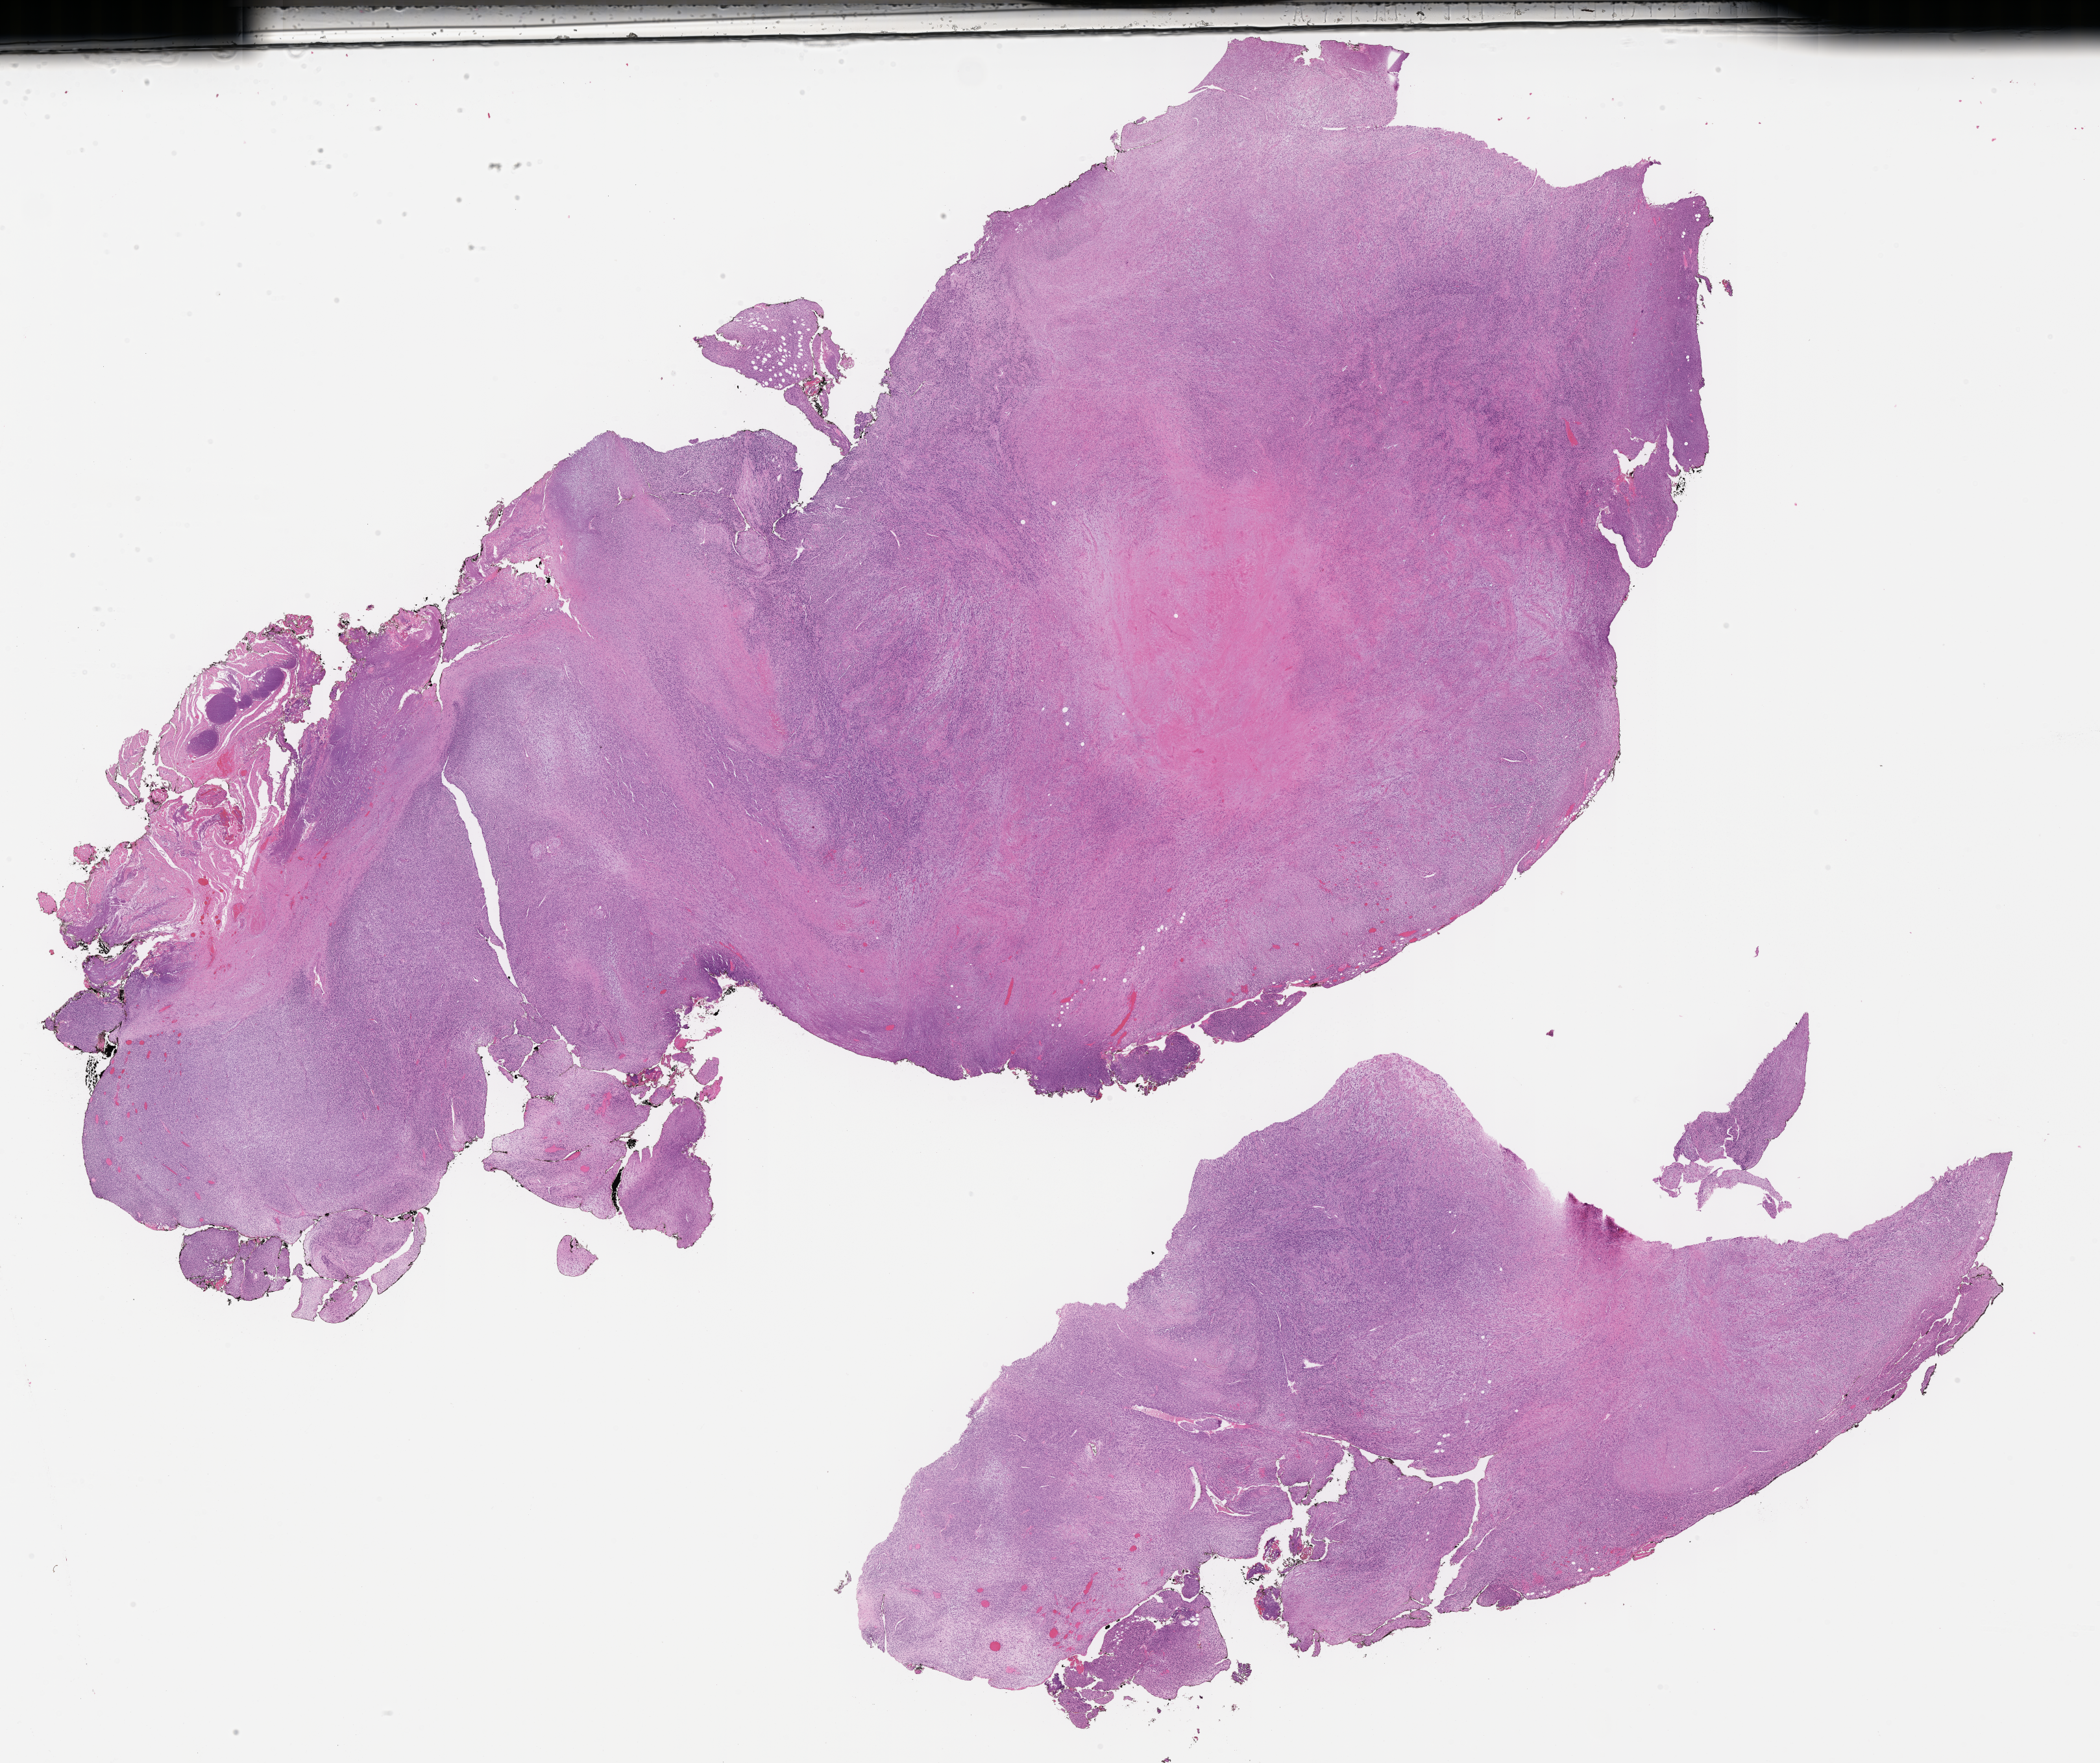
Hematoxylin and eosin (H&E) whole-slide image of tumor tissue — whole scanned area (about 26.2 x 22.0 mm) shown as a low-resolution overview; FFPE section; site: bone Marrow. Patient: male, age 3.5 years at diagnosis.
* metastatic status at presentation (as recorded): non-metastatic (confirmed)
* stage (as recorded): 2
* diagnosis: rhabdomyosarcoma; histological classification: spindle cell rhabdomyosarcoma